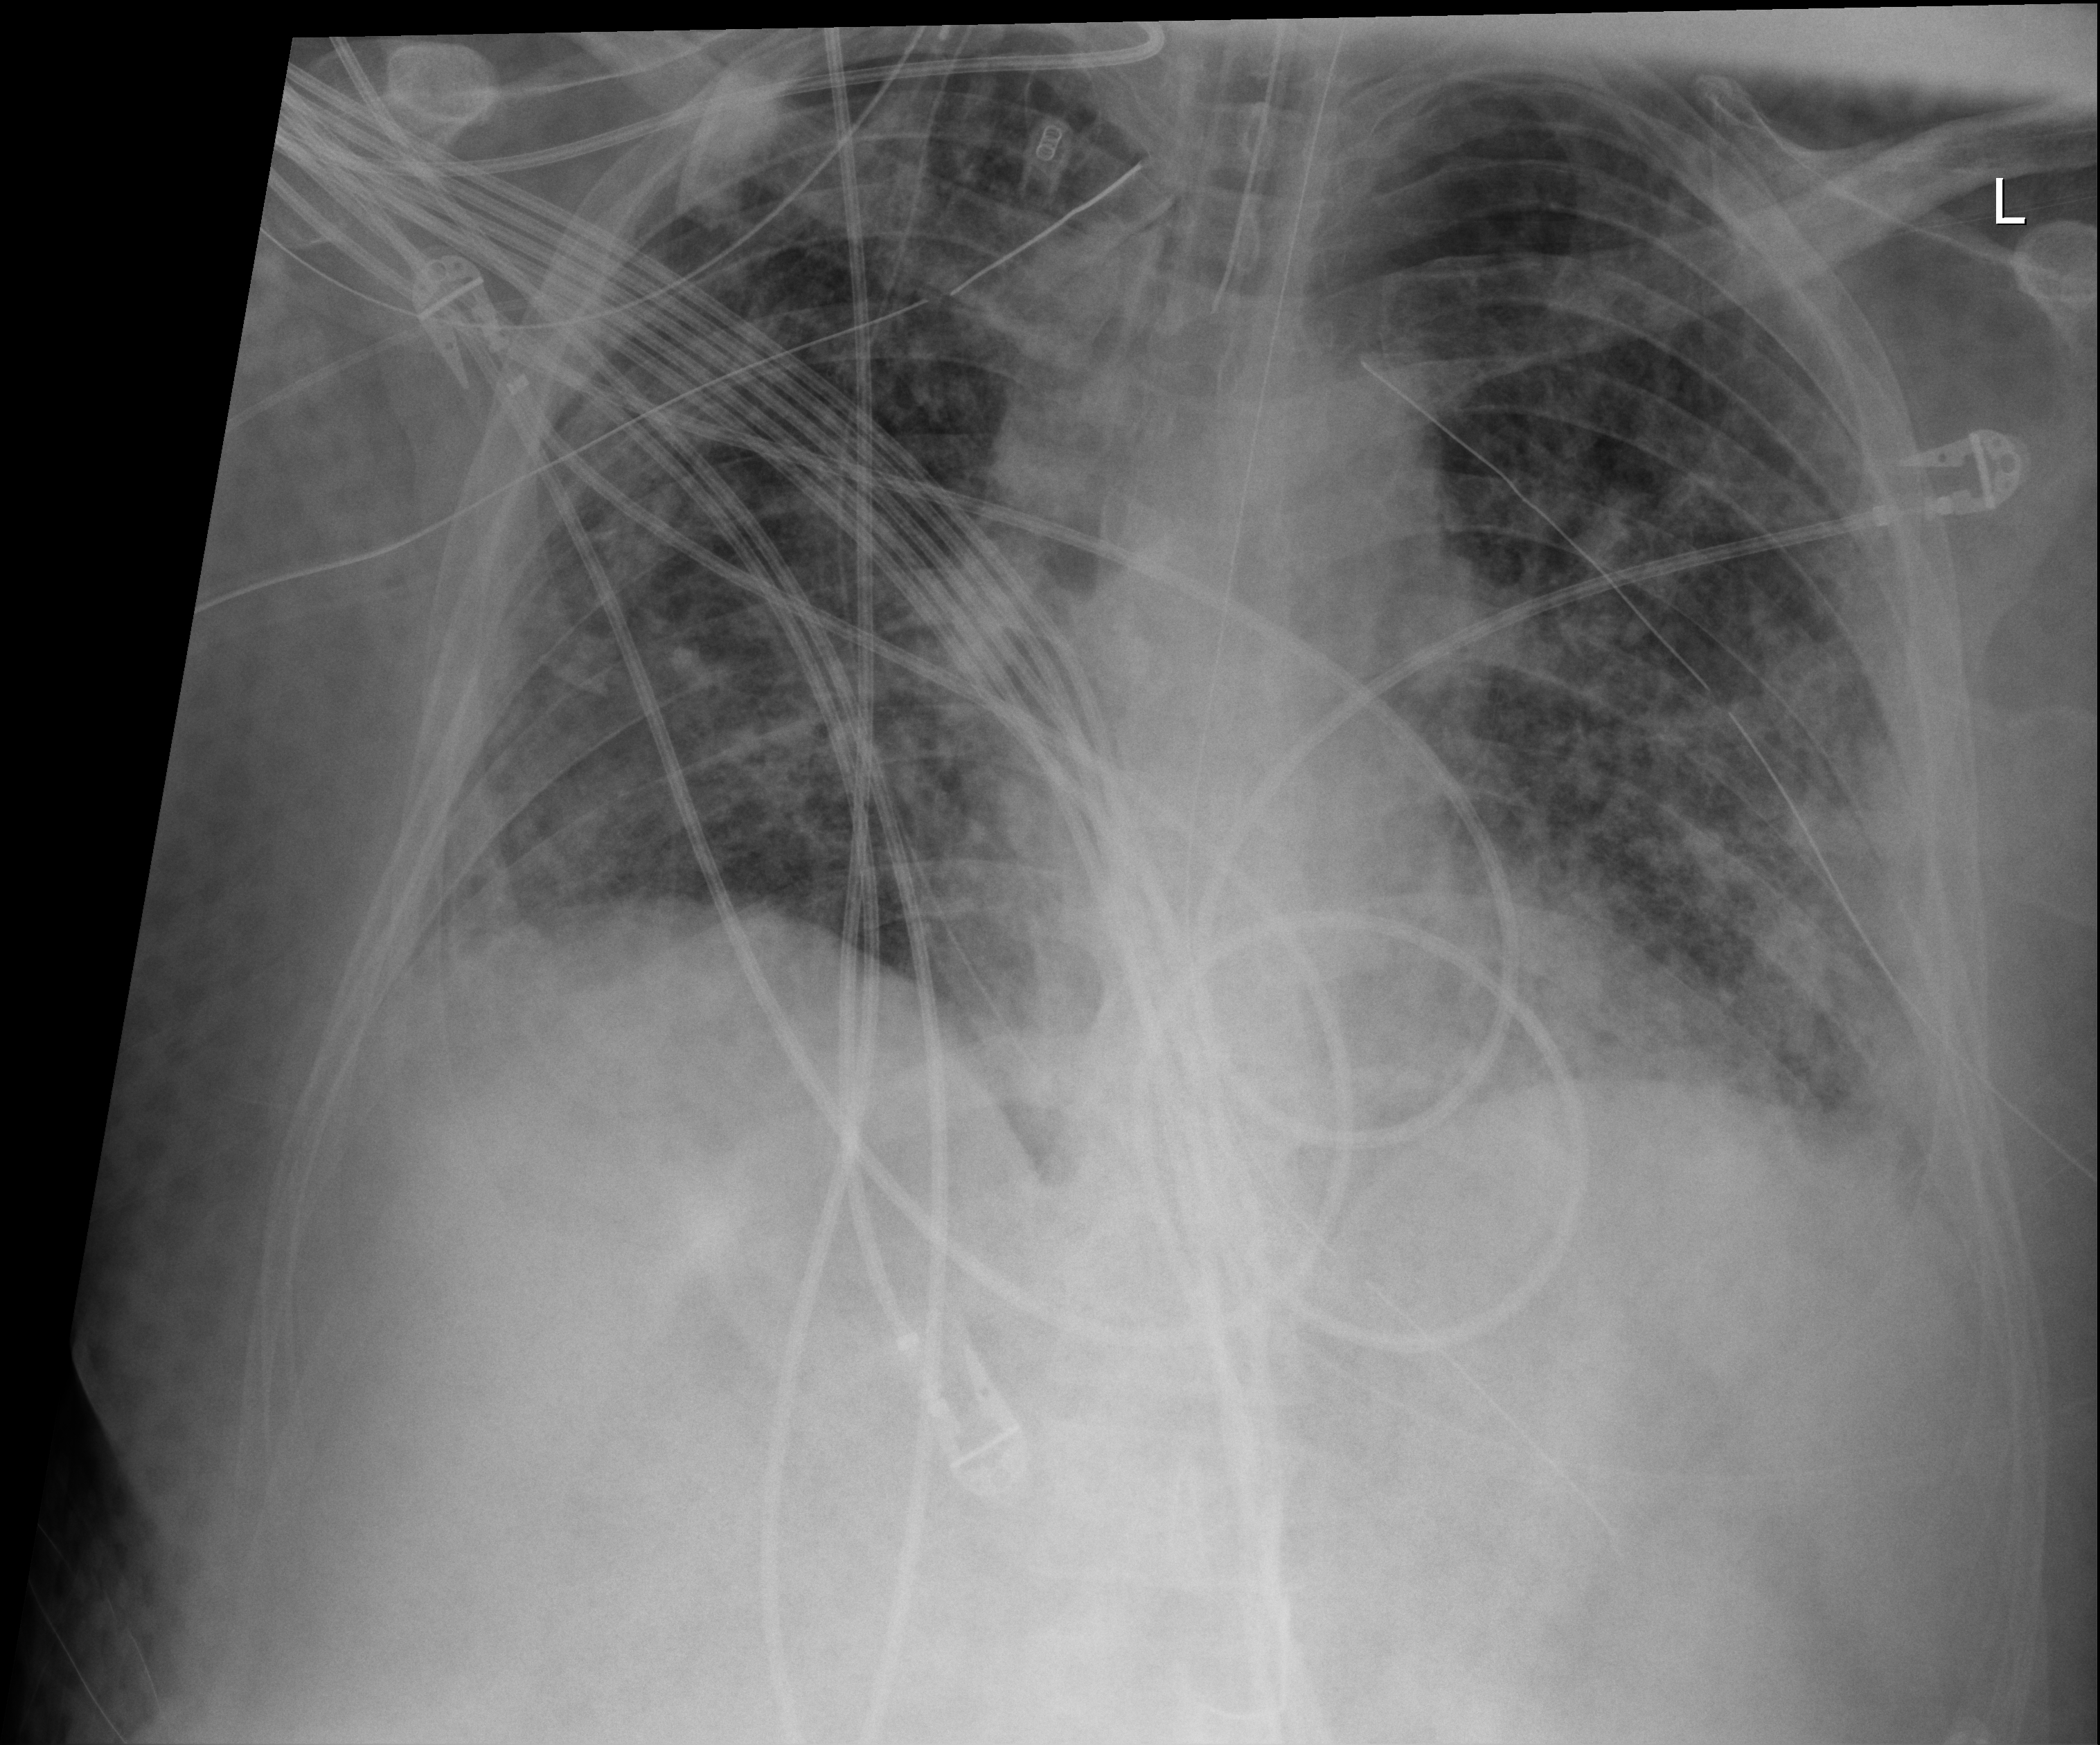
Chest X-ray (portable), anteroposterior (AP) projection. Male patient hospitalised with COVID-19, age 18–59 years.
Admission-level facts for this patient (not findings on this image; timing relative to this image not recorded): admitted to intensive care during this hospital stay: yes.